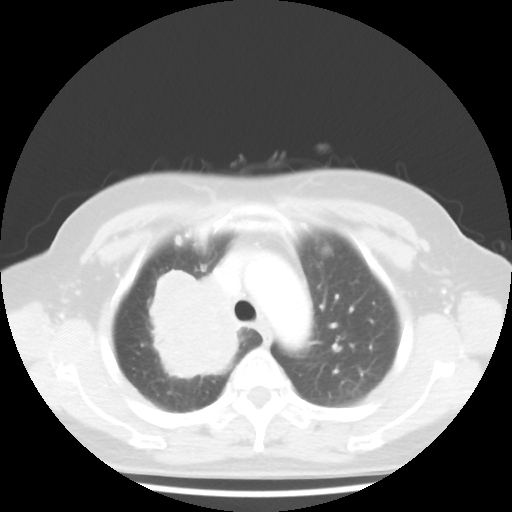
Chest CT, one axial slice; slice 34 of 44 in the series (ordered by position); 100 kVp; lung window (W 1500 / L -600 HU); 5 mm slice thickness; 512 × 512 image matrix, field of view 316 × 316 mm. Patient: female, 62 years. Case-level facts recorded for this patient, not image findings: clinical TNM (as recorded): T3 N0 M0; histopathological grade: G3.
Structures marked on this image (rectangle marked by the reading radiologist):
- lung tumour (recorded histology: small cell carcinoma): bounding box [x1, y1, x2, y2] px = [146, 266, 253, 386]